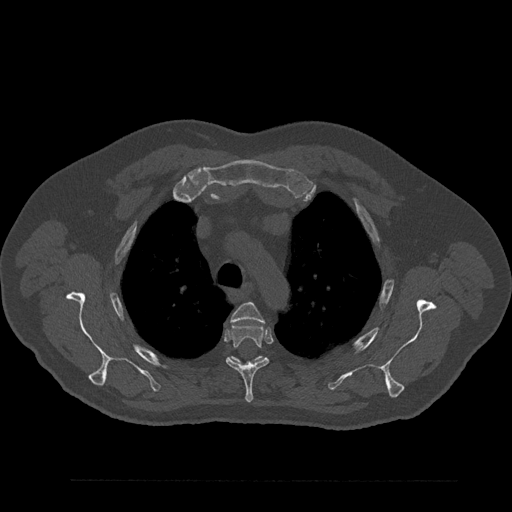
CT including the spine, one axial slice; position 644 of 797 along the scan axis; 120 kVp; bone window (W 1800 / L 400 HU); 0.5 mm slice thickness; 512 × 512 image matrix, field of view 430 × 430 mm. Patient: male, 61 years. From the clinical record (not read from this slice): primary cancer: prostate.
Annotated regions visible in this slice (semi-automatically segmented with operator editing):
- T3 vertebra: bounding box <231,302,264,323> (left, top, right, bottom; pixels)
- T4 vertebra: <225,324,269,403>
- T5 vertebra: <231,356,265,365>